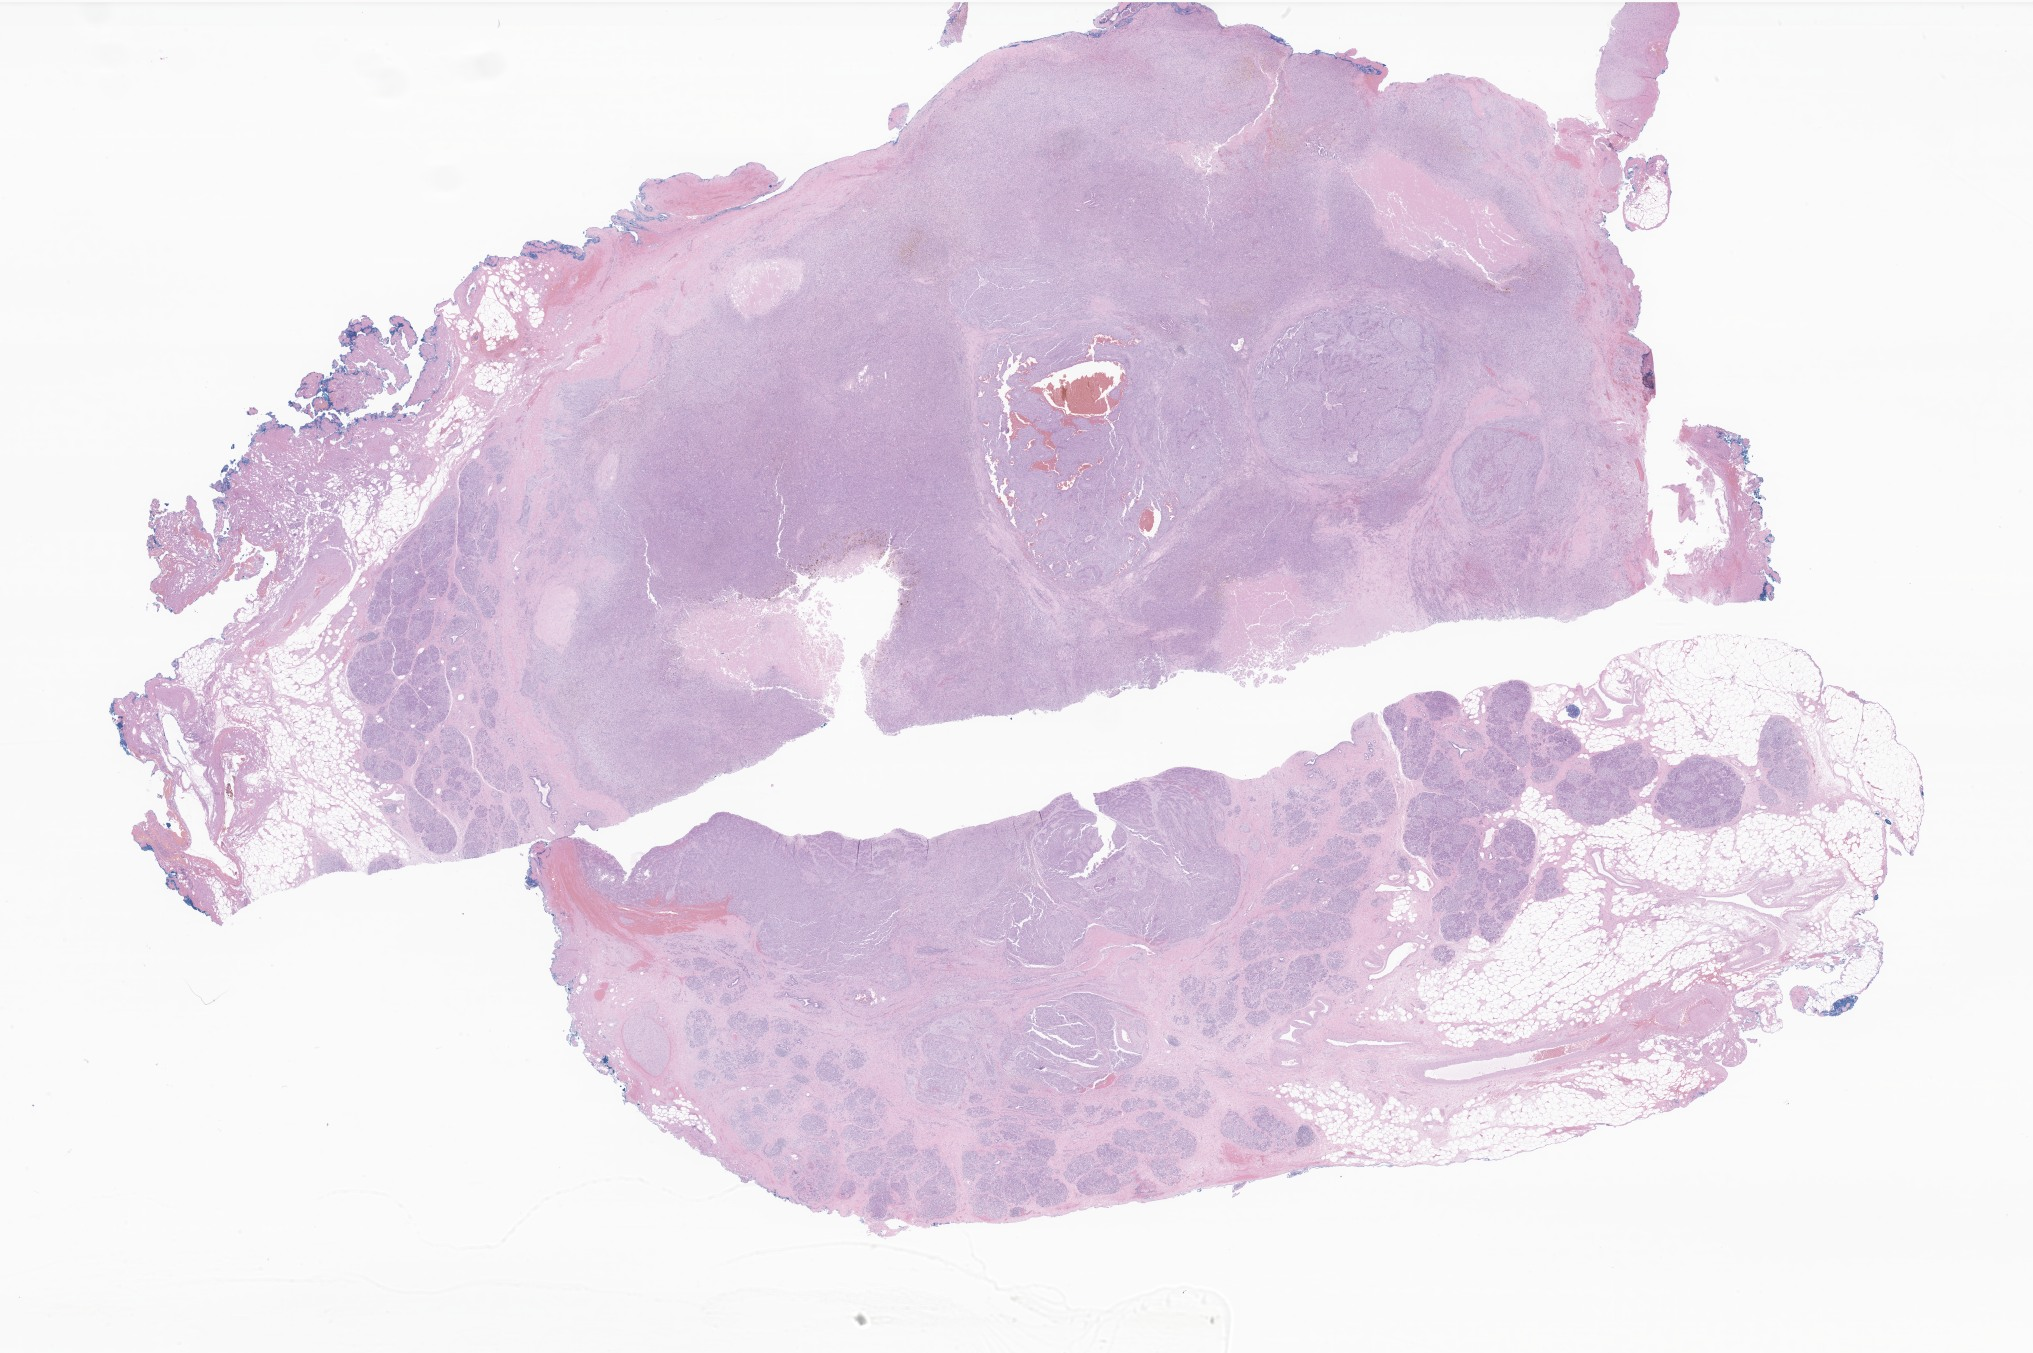
Haematoxylin and eosin whole-slide image of tumor tissue from the pancreas, whole scanned area (about 34.3 x 22.8 mm) shown as a low-resolution overview, formalin-fixed, paraffin-embedded (FFPE) tissue. Patient: female, age 124 months (10 years 4 months).
Recorded diagnosis: Neoplasm, malignant.